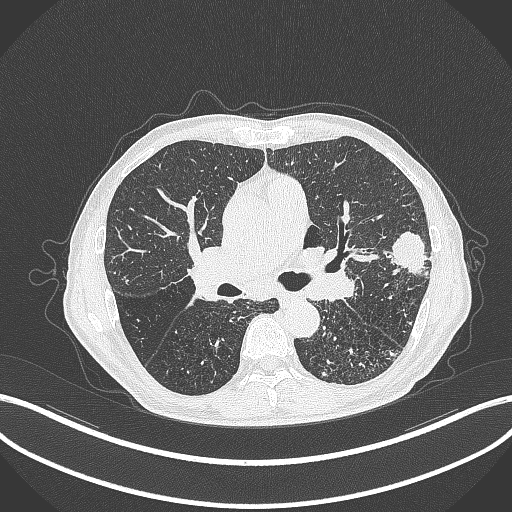
Chest CT, one axial slice. Slice 241 of 463 in the series (ordered by position). Reconstruction kernel B70f. Lung window (W 1500 / L -600 HU). 1 mm slice thickness. 512 × 512 image matrix, field of view 400 × 400 mm. Patient: male, 74 years. From the clinical record (not read from this slice): clinical TNM (as recorded): T2a N1 M0.
Annotated regions visible in this slice (bounding box drawn by a radiologist):
- lung tumour (recorded histology: adenocarcinoma): bounding box [x1, y1, x2, y2] px = [383, 230, 429, 284]